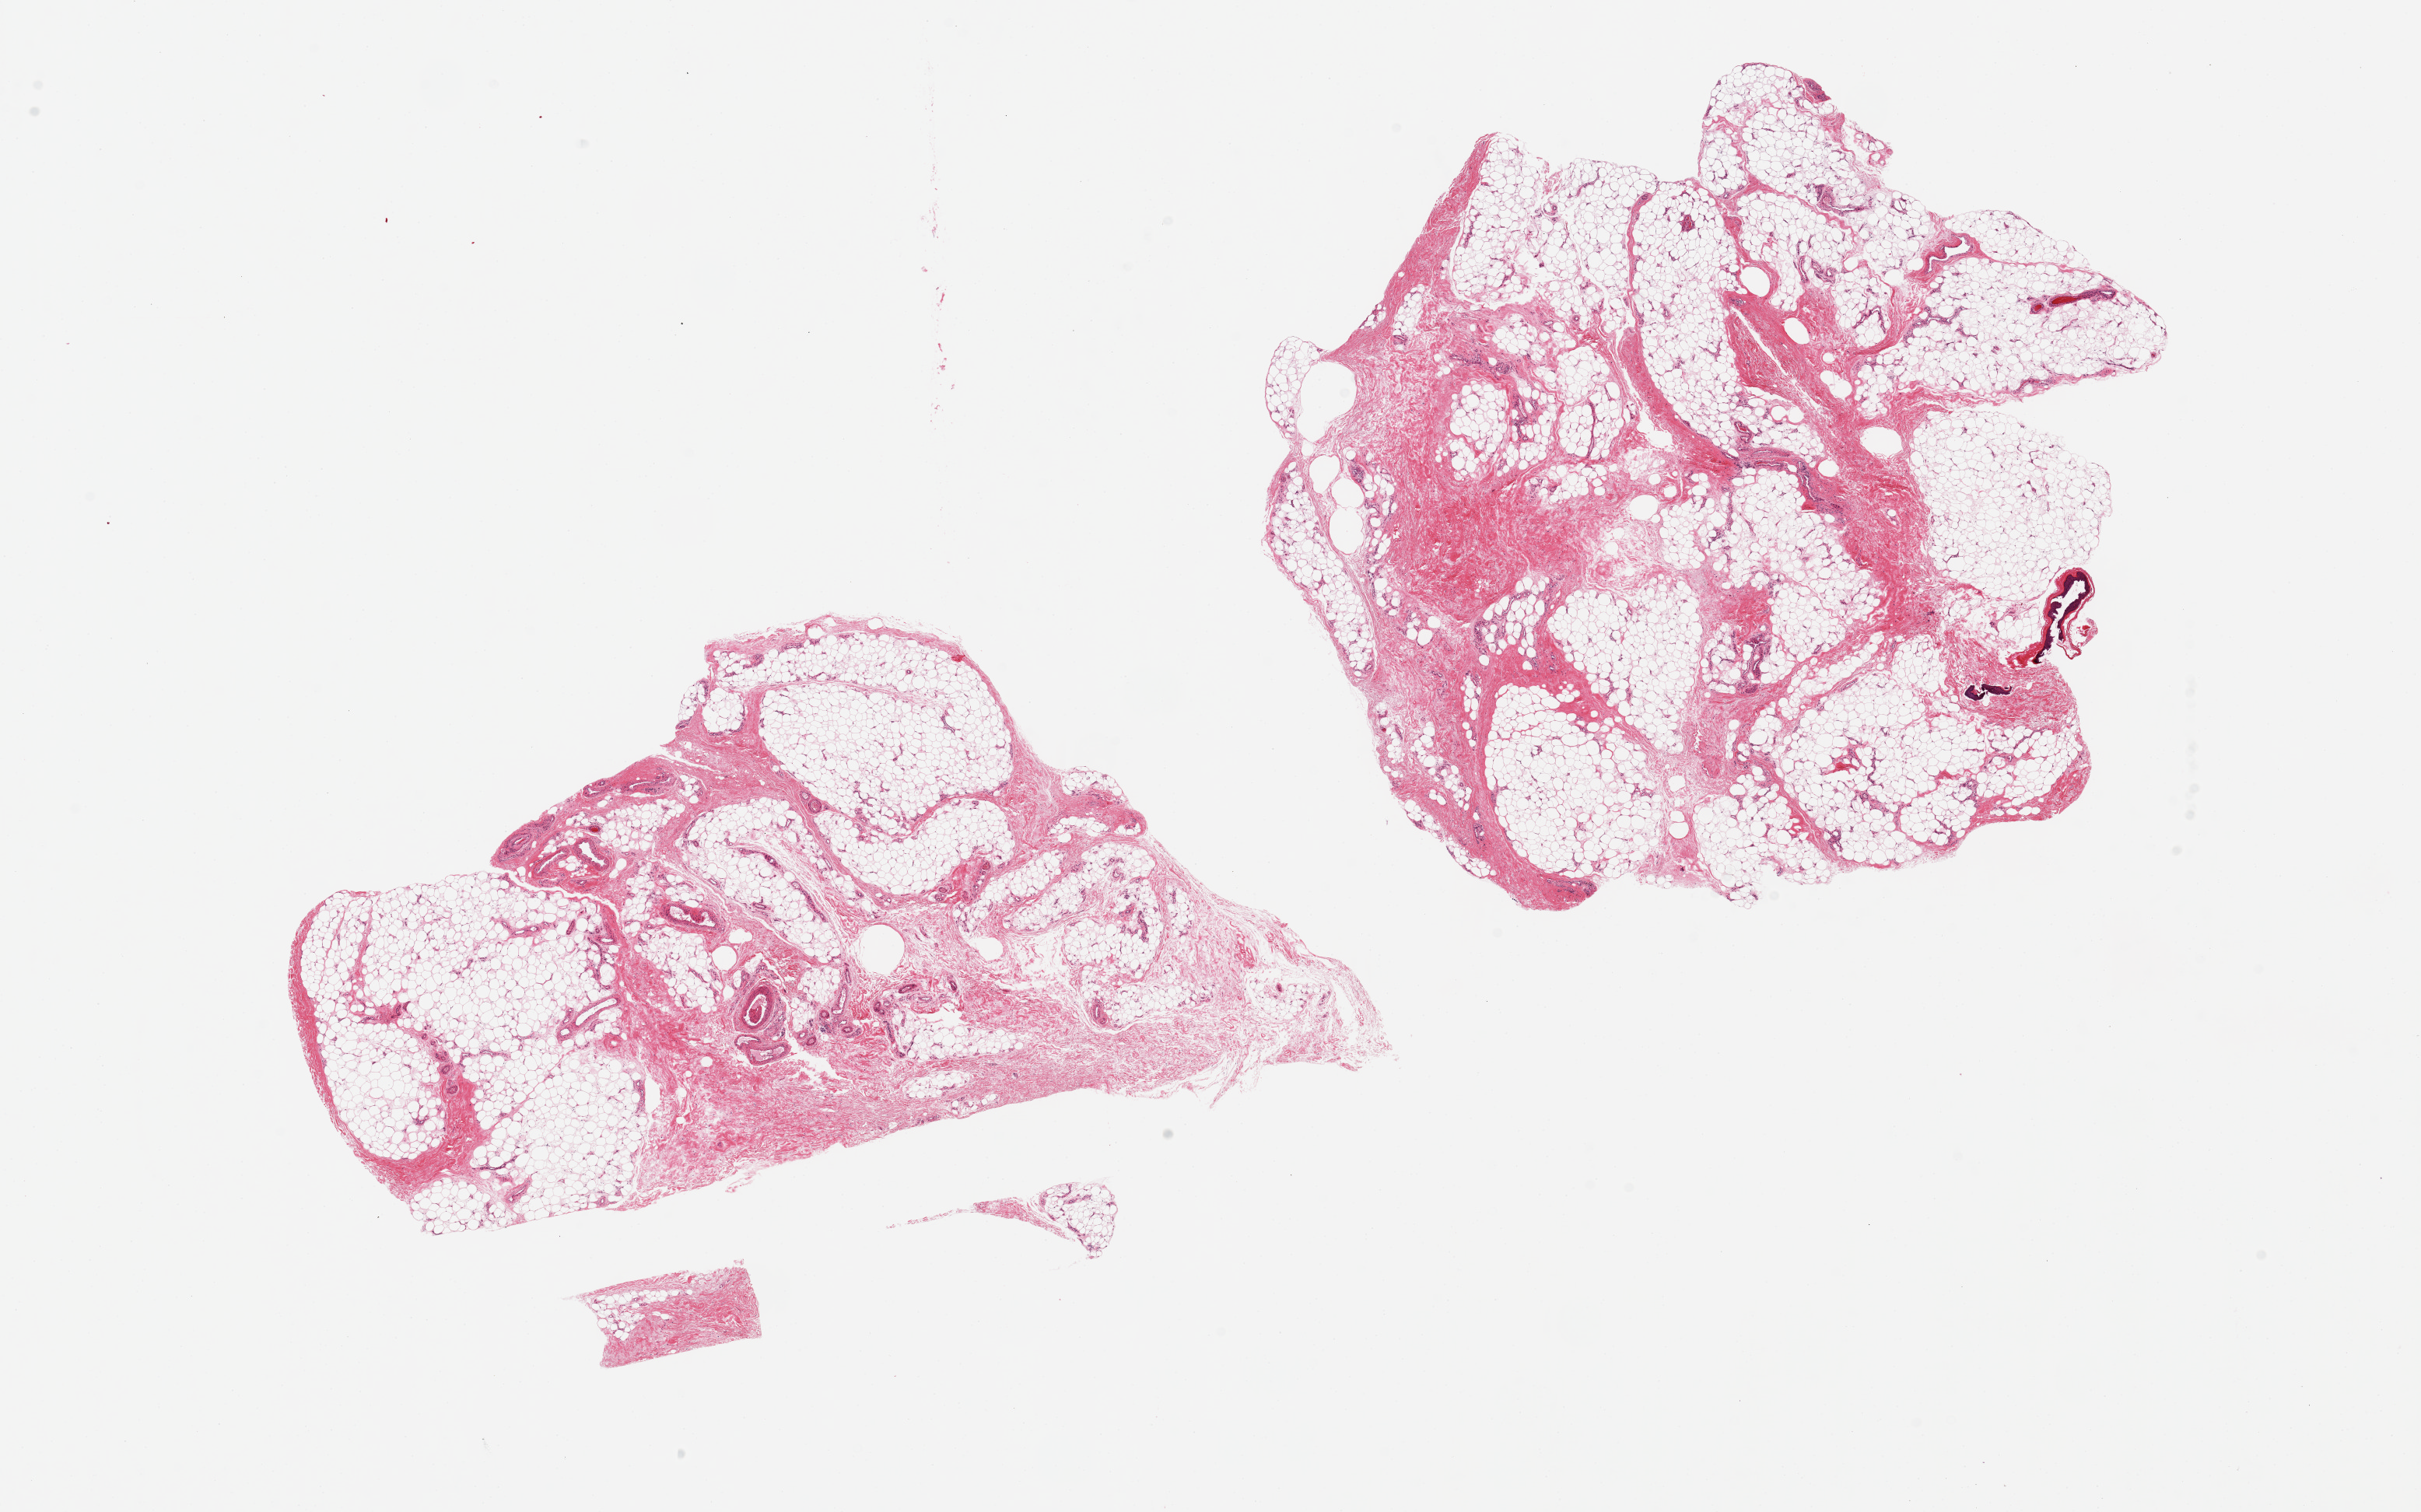
Whole-slide image, hematoxylin and eosin (H&E) stain, brightfield — shown as a low-resolution overview of the whole scanned area (about 24.6 x 15.4 mm); PAXgene-fixed, paraffin-embedded tissue; section of adipose tissue (target tissue); donor tissue sample.
Pathologist's review note for this sample: 2 pieces, 8x6 & 9x8mm; 50% fibirous tissue; Contaminant squamous epithelium.